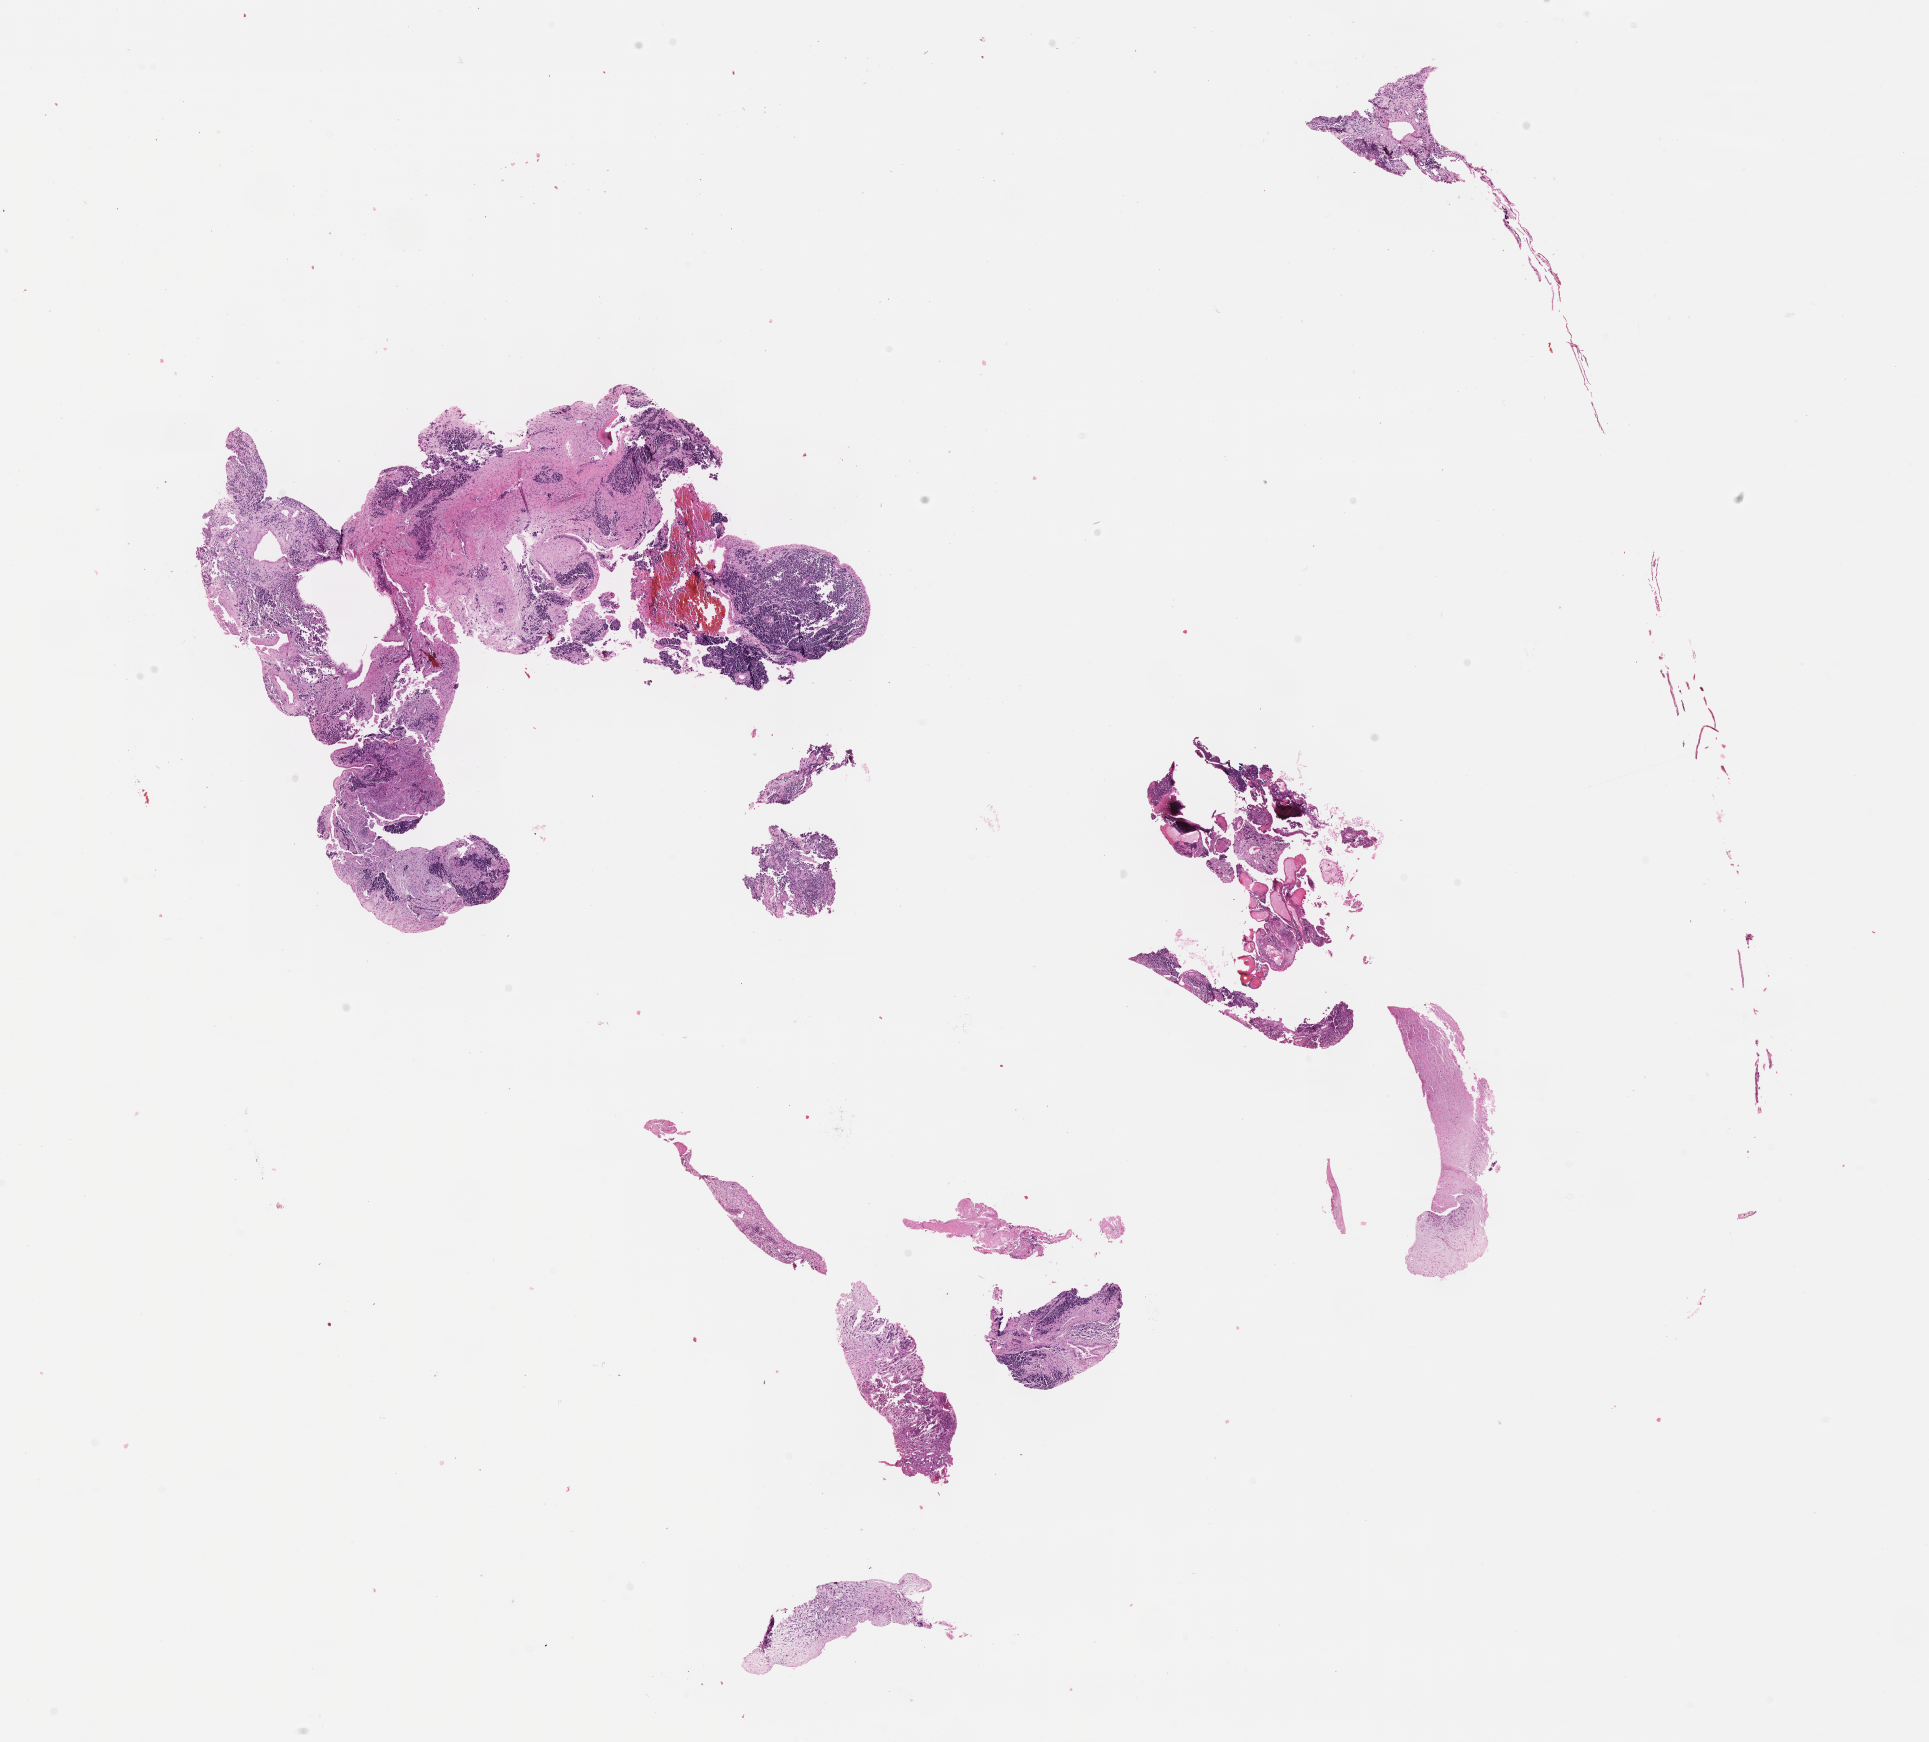
Digitized haematoxylin and eosin-stained section of tumor tissue, low-resolution overview of the scanned area, about 15.6 x 14.1 mm. Formalin-fixed paraffin-embedded section. Sample anatomic site: nasal cavity. Patient: male, age 13.6 years at diagnosis.
- diagnosis: rhabdomyosarcoma; histological classification: alveolar rhabdomyosarcoma
- stage (as recorded): 4
- metastatic status at presentation (as recorded): metastatic (confirmed)